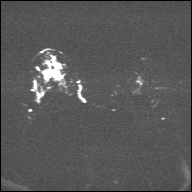
Breast MRI, one axial slice. Diffusion-weighted series; image 2 of 4 stored at this slice position (different b-values; order by instance number). 1.5 T. 4 mm slice thickness. 192 × 192 image matrix, field of view 360 × 360 mm. Female patient.
Structures marked on this image (expert manual segmentation):
- tumour on diffusion-weighted imaging: bounding box (x1, y1, x2, y2) in pixels: (50, 70, 56, 77)